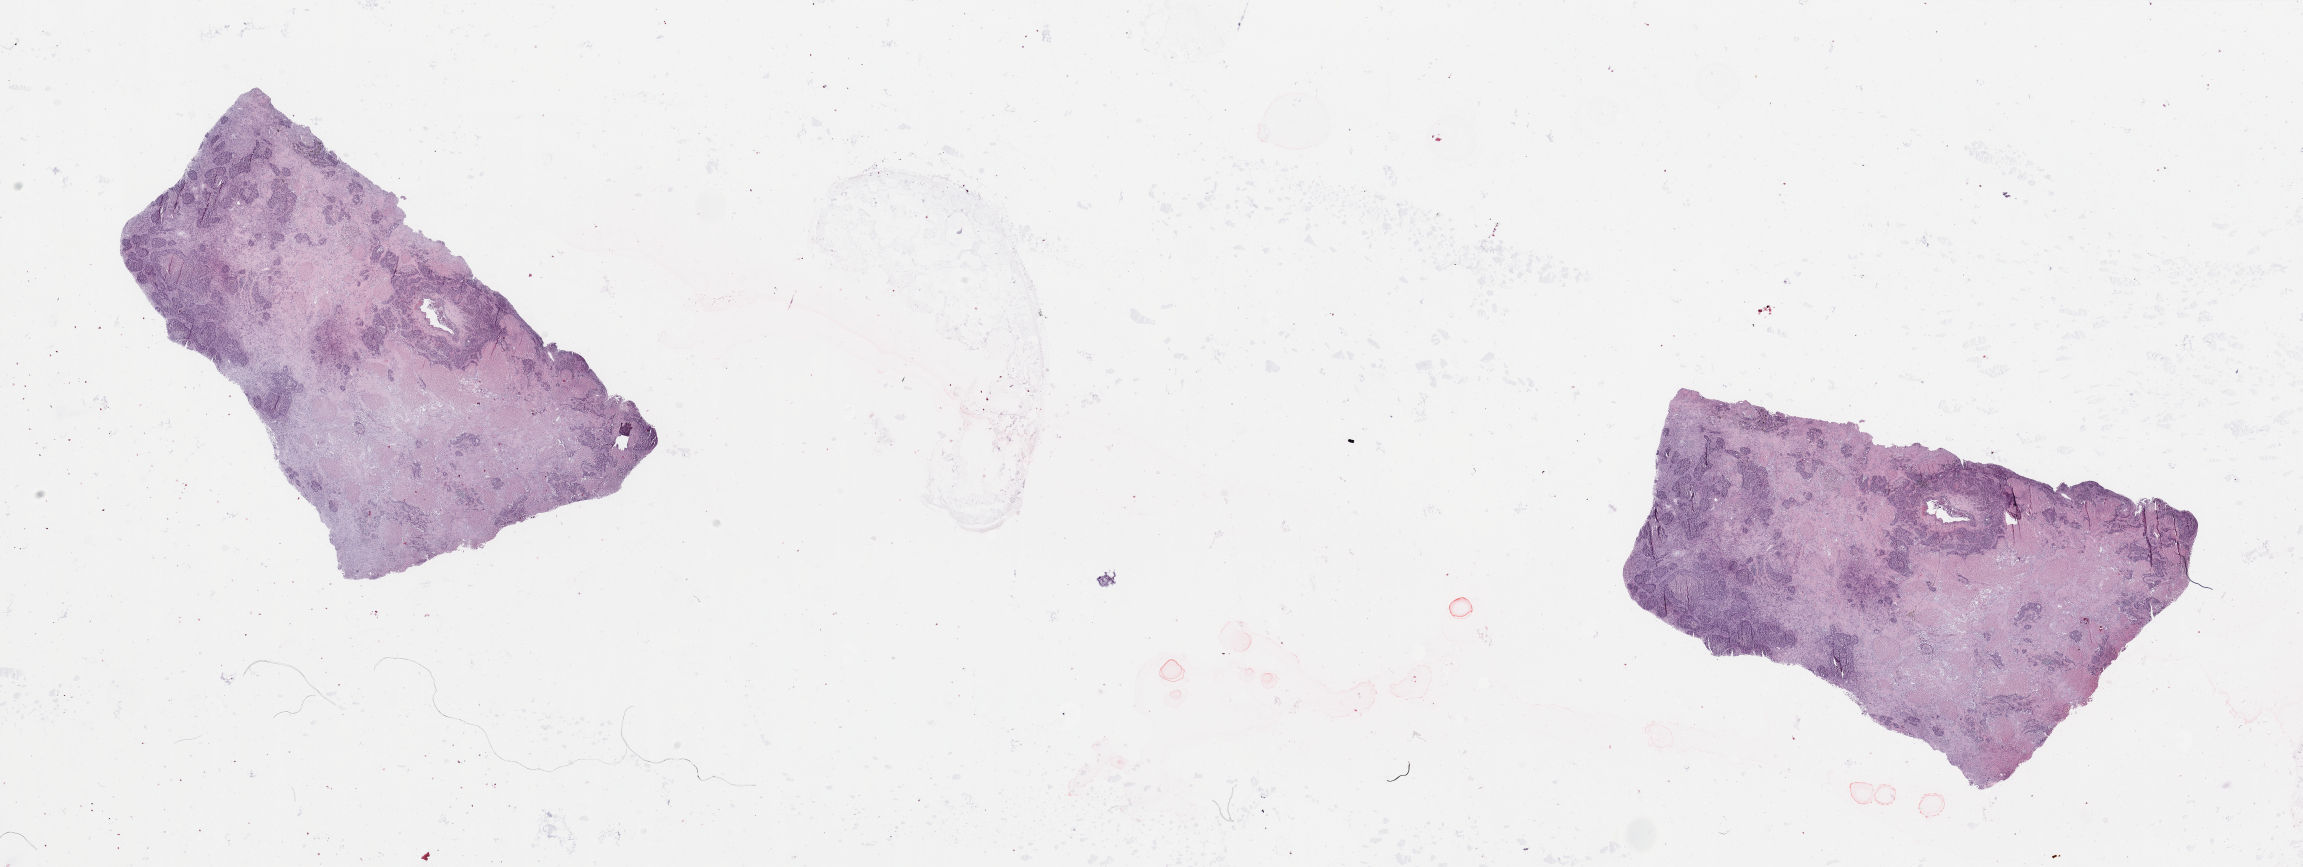
Digitized H&E-stained tissue section (whole slide), whole scanned area (about 36.4 x 13.7 mm, slide scanned at 20x) shown as a low-resolution overview, lung, tumour tissue. 62-year-old male patient. Histologic grade: G3 (poorly differentiated).
- primary tumour site (as recorded): left lower lobe
- AJCC pathologic stage: IIIB
- diagnosis: Squamous cell carcinoma, NOS